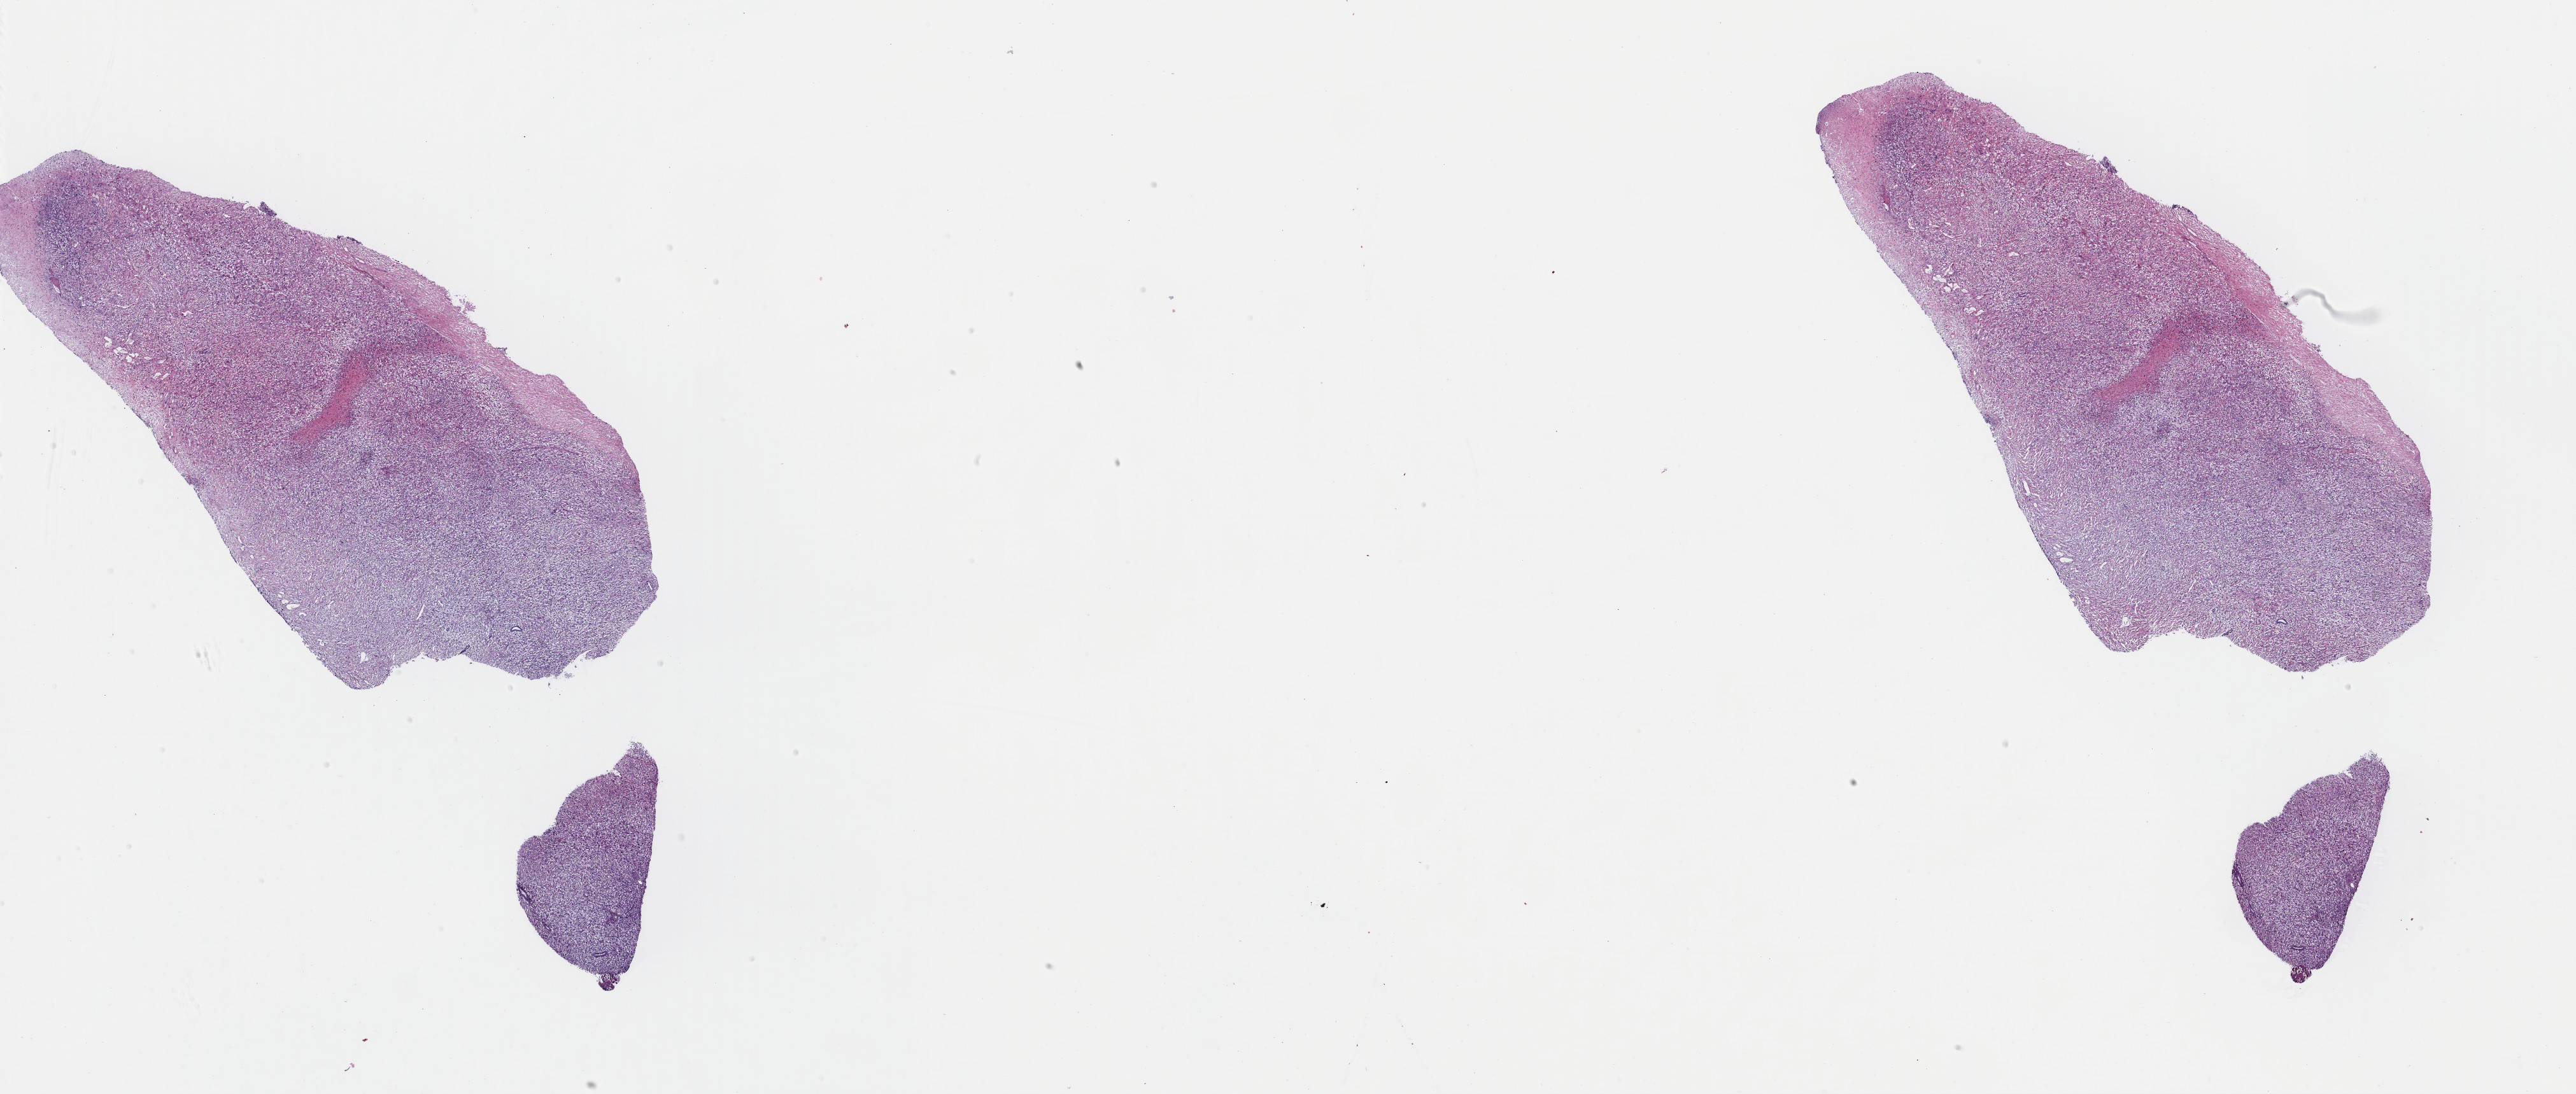
Digitized Hematoxylin and eosin (H&E) stained tissue section (whole slide), shown as a low-resolution overview of the whole scanned area (about 32.0 x 13.6 mm), formalin-fixed paraffin-embedded (FFPE) diagnostic section, primary tumour sample from the uterus. Female patient; age at initial diagnosis 71 years.
Diagnosis: Leiomyosarcoma, NOS.